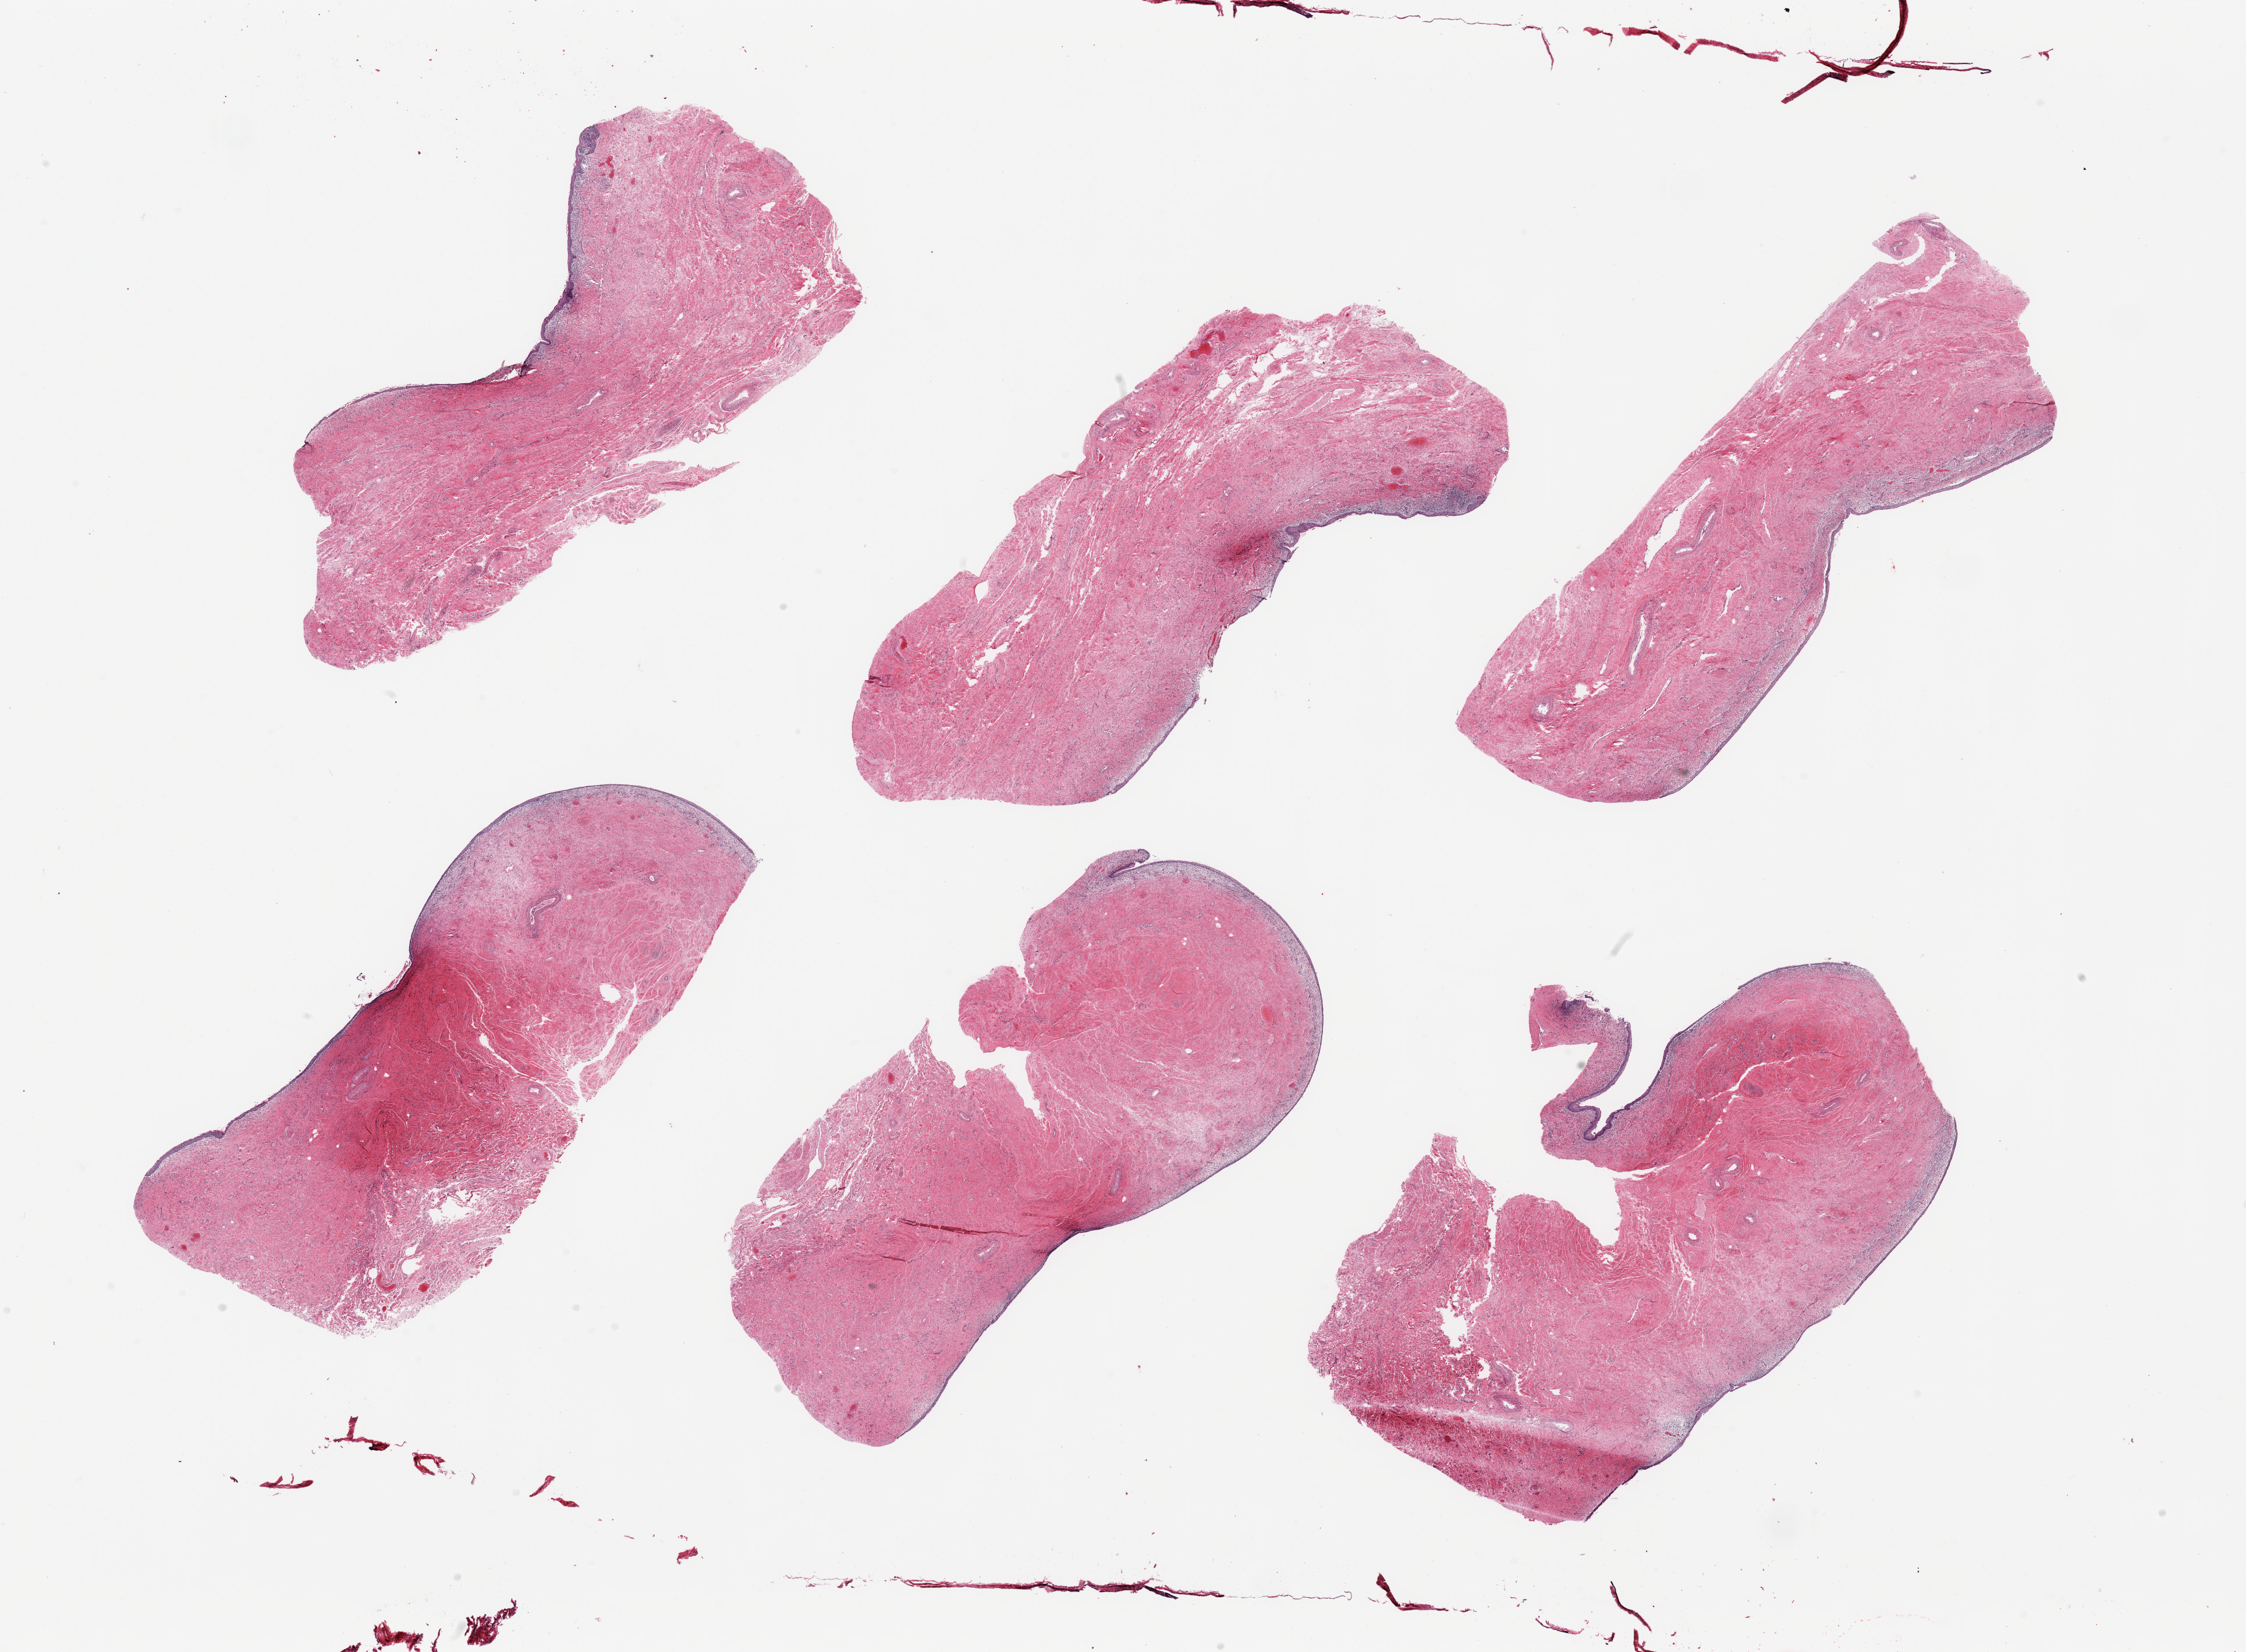
Digitized H&E-stained section, low-resolution overview of the scanned area, about 30.5 x 22.5 mm (acquisition: 20x scan); PAXgene-fixed paraffin-embedded (PFPE) section; target tissue: vagina; tissue donor sample. Female donor.
Review note (as recorded): 6 pieces, squmaous mucosa present, focal chronic vaginaitis.